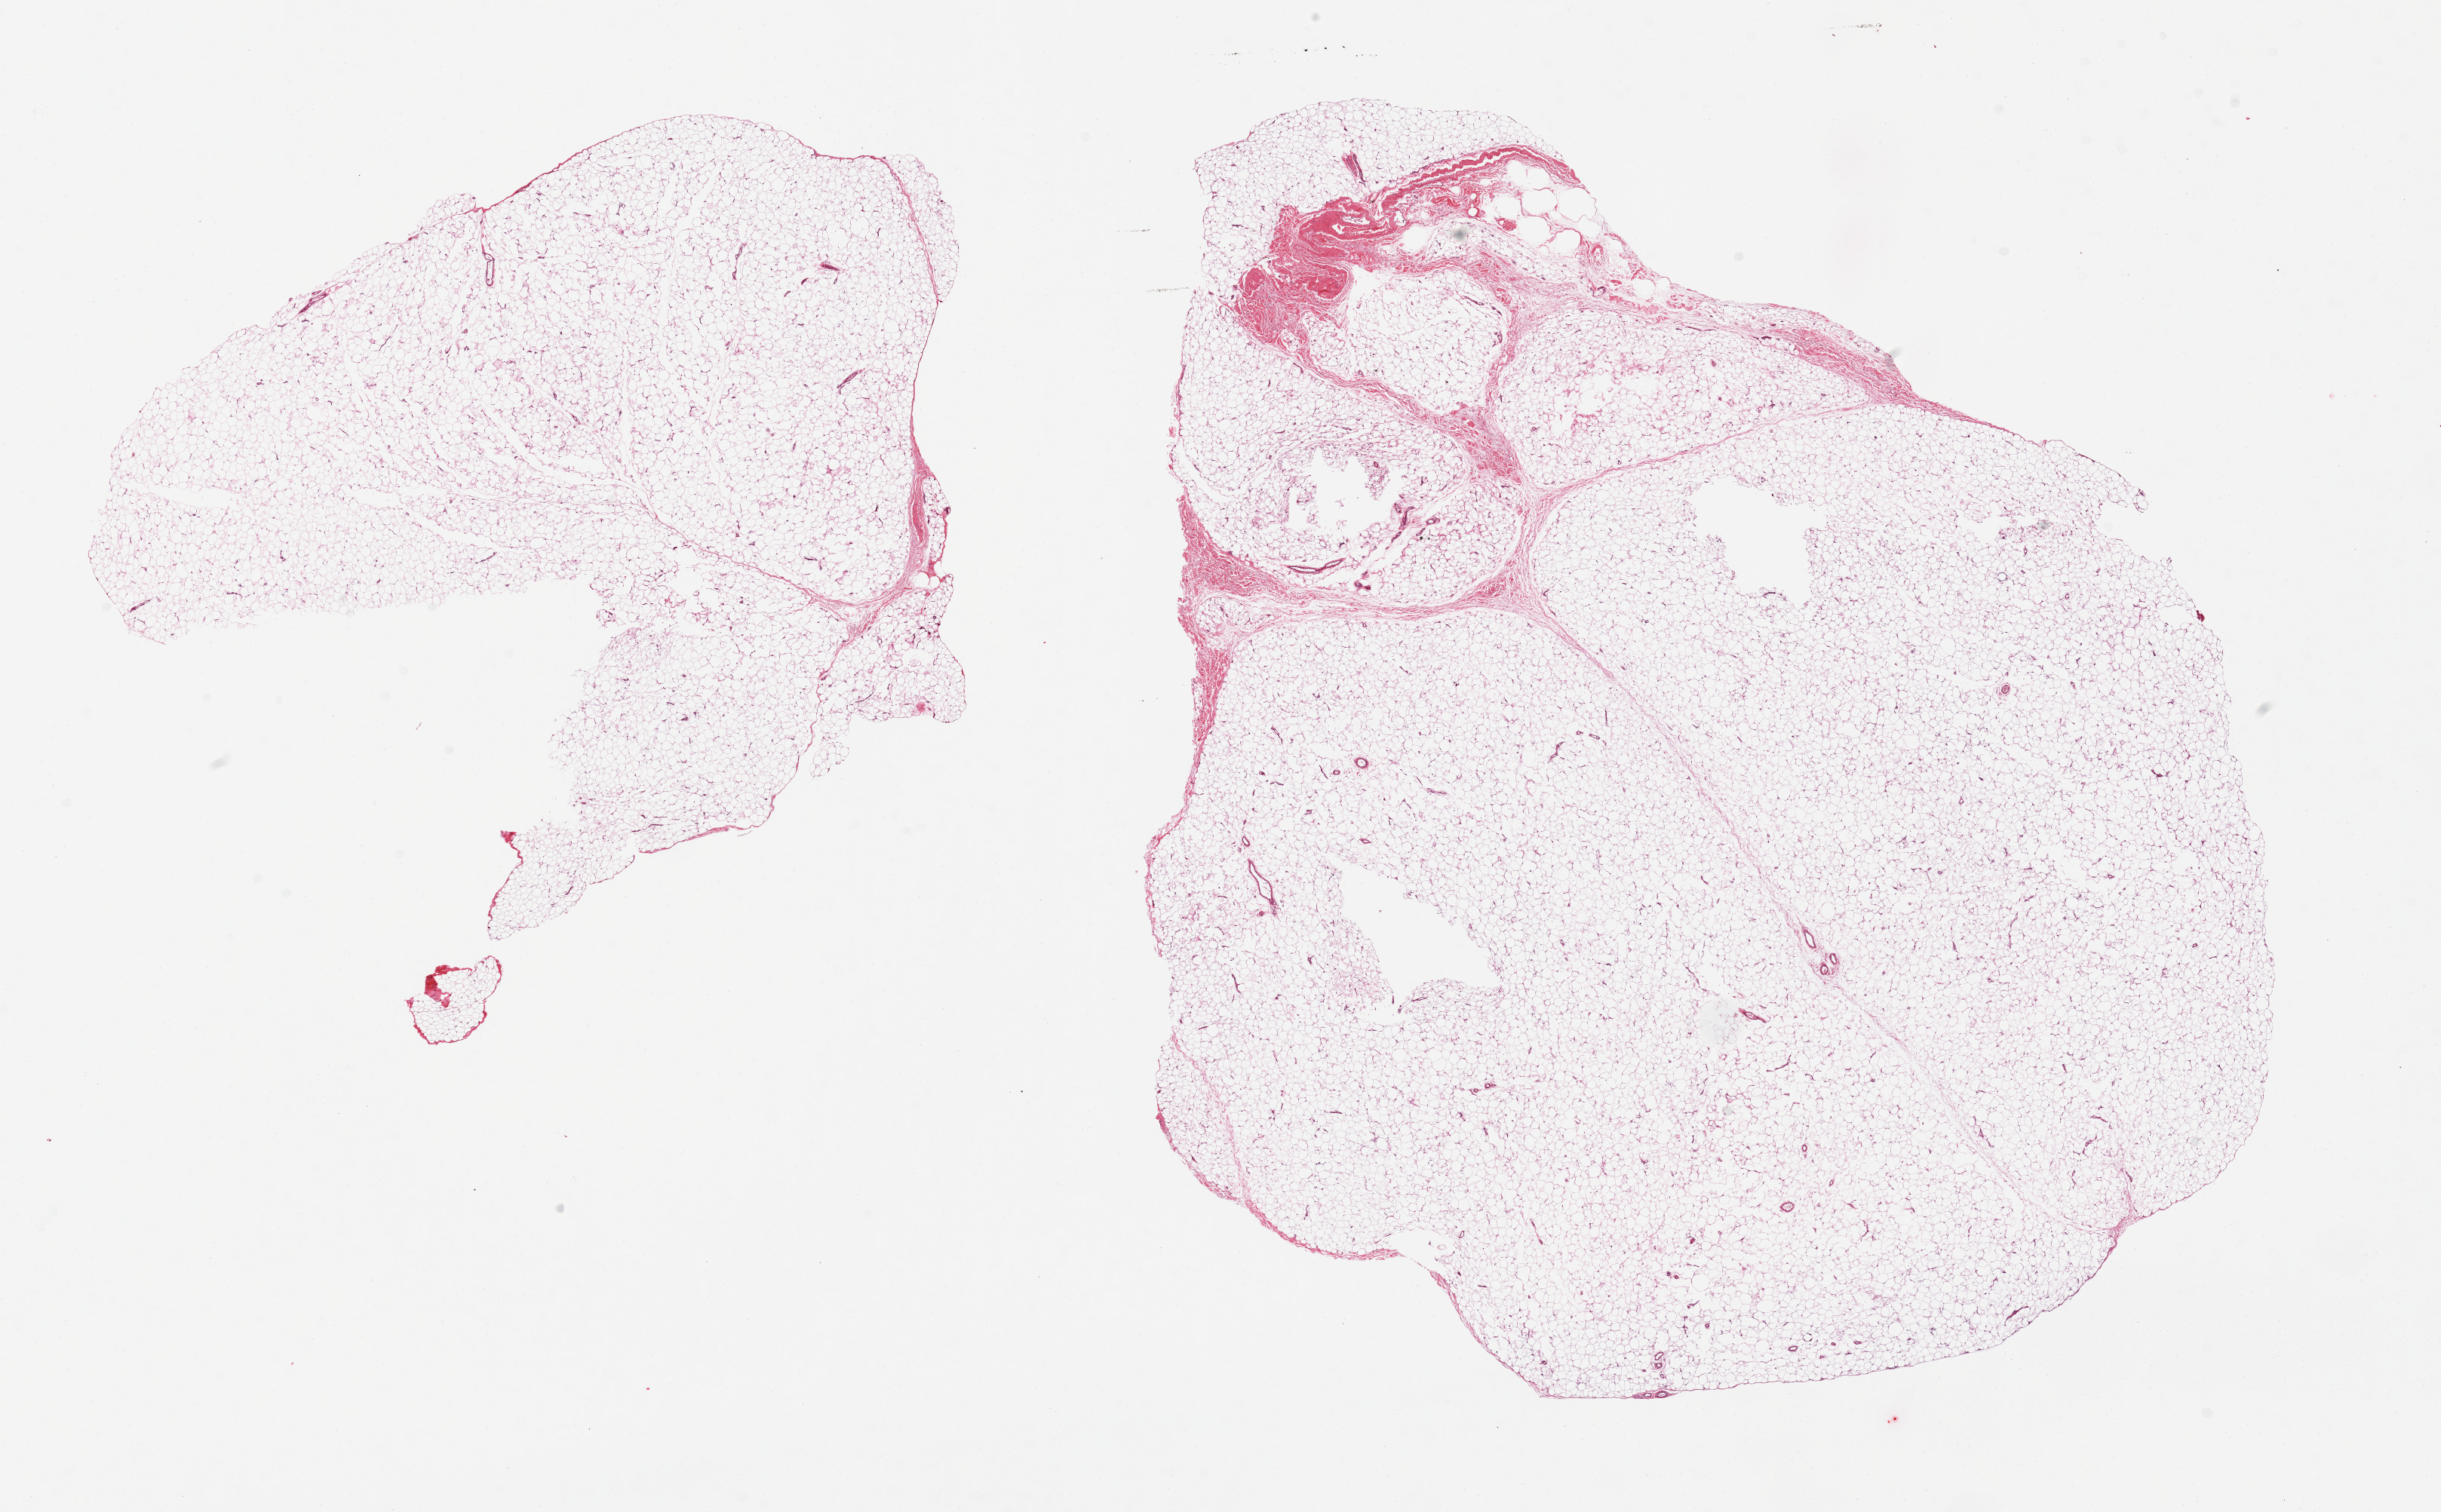
Whole-slide image, hematoxylin and eosin (H&E) stain, whole scanned area (about 25.6 x 15.9 mm, from a 20x scan) shown as a low-resolution overview; PAXgene-fixed, paraffin-embedded tissue; target tissue: adipose tissue; tissue donor sample.
• review note (as recorded): 2 pieces, ~5% fascia/vascular tissue